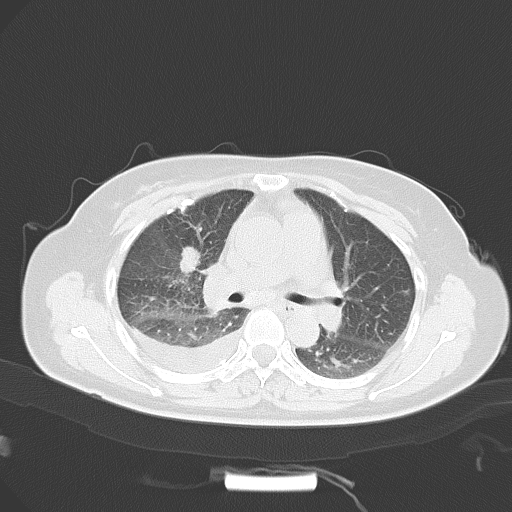
Chest CT, one axial slice. Position 22 of 41 along the scan axis. Reconstruction kernel B70f. 120 kVp. Lung window (W 1500 / L -600 HU). 5 mm slice thickness. 512 × 512 image matrix, field of view 360 × 360 mm. Female patient, age 53 years. Case-level facts recorded for this patient, not image findings: clinical TNM (as recorded): T1c N1 M1b.
Outlined on this slice (rectangle marked by the reading radiologist):
- lung tumour (recorded histology: adenocarcinoma): bounding box <178,242,203,278> (left, top, right, bottom; pixels)